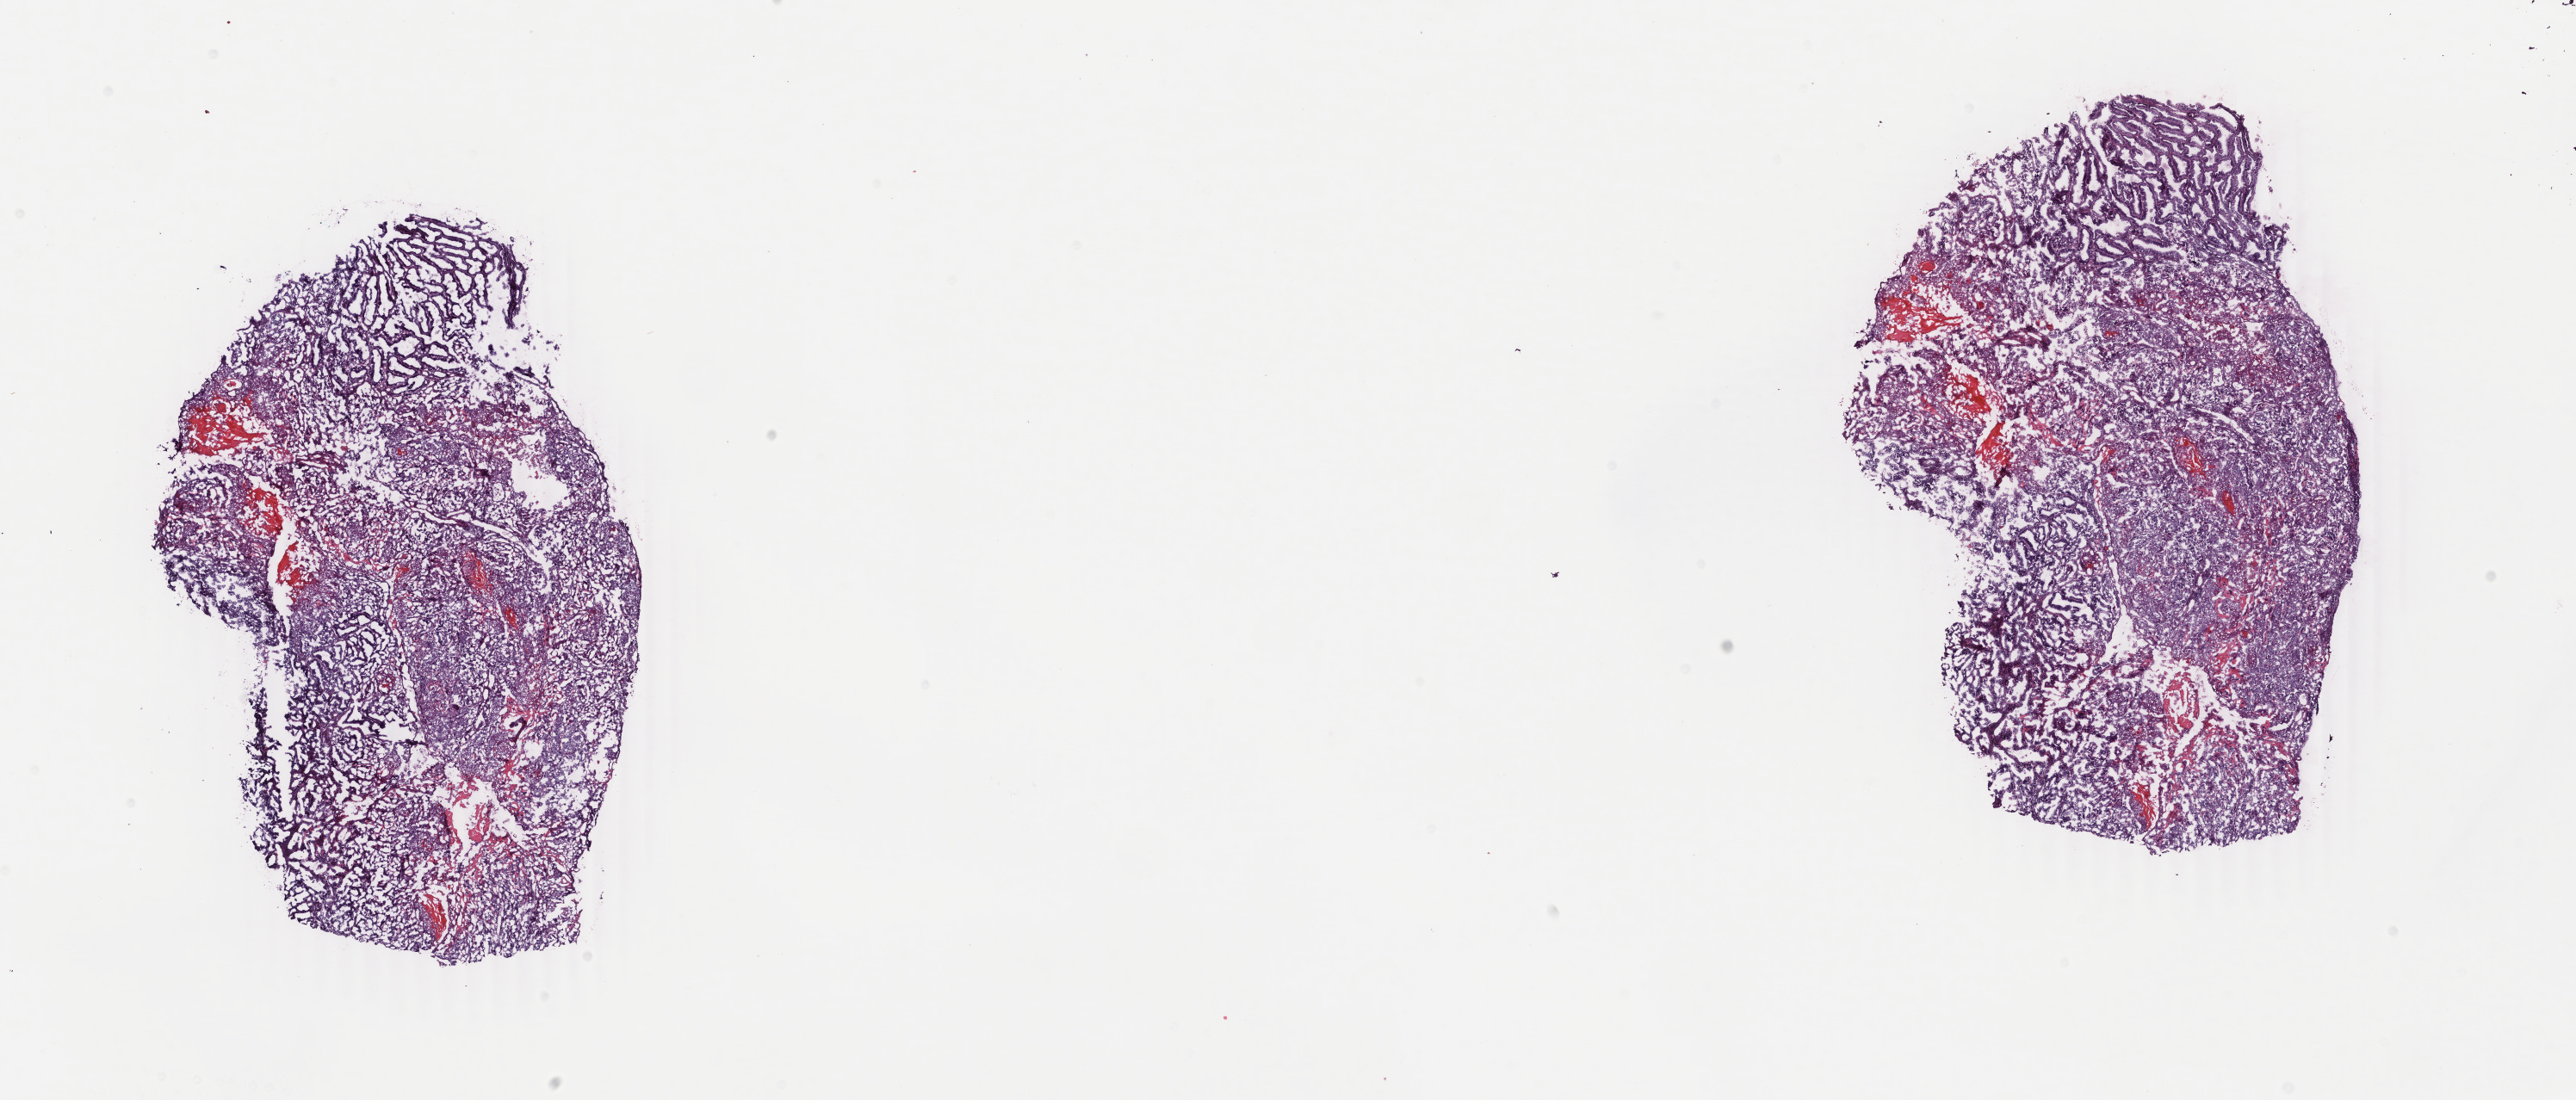
Whole-slide histology image, Hematoxylin and eosin (H&E) stained — a low-resolution overview of the entire scanned area, about 23.8 x 10.2 mm, frozen section from the bottom of the tissue portion, primary tumour sample from the uterus. Female patient; age at initial diagnosis 39 years. Histologic grade: G3 (poorly differentiated). Slide review estimates, as recorded: tumour cells 80%, tumour nuclei 80%, normal cells 0%, stromal cells 15%, necrosis 5%. Inflammatory infiltration, as recorded: lymphocyte infiltration 40%, monocyte infiltration 10%, neutrophil infiltration 30%.
Diagnosis: Endometrioid adenocarcinoma, NOS (endometrium). Lymph nodes positive (case pathology): 1 of 2 examined. FIGO stage: IVB.